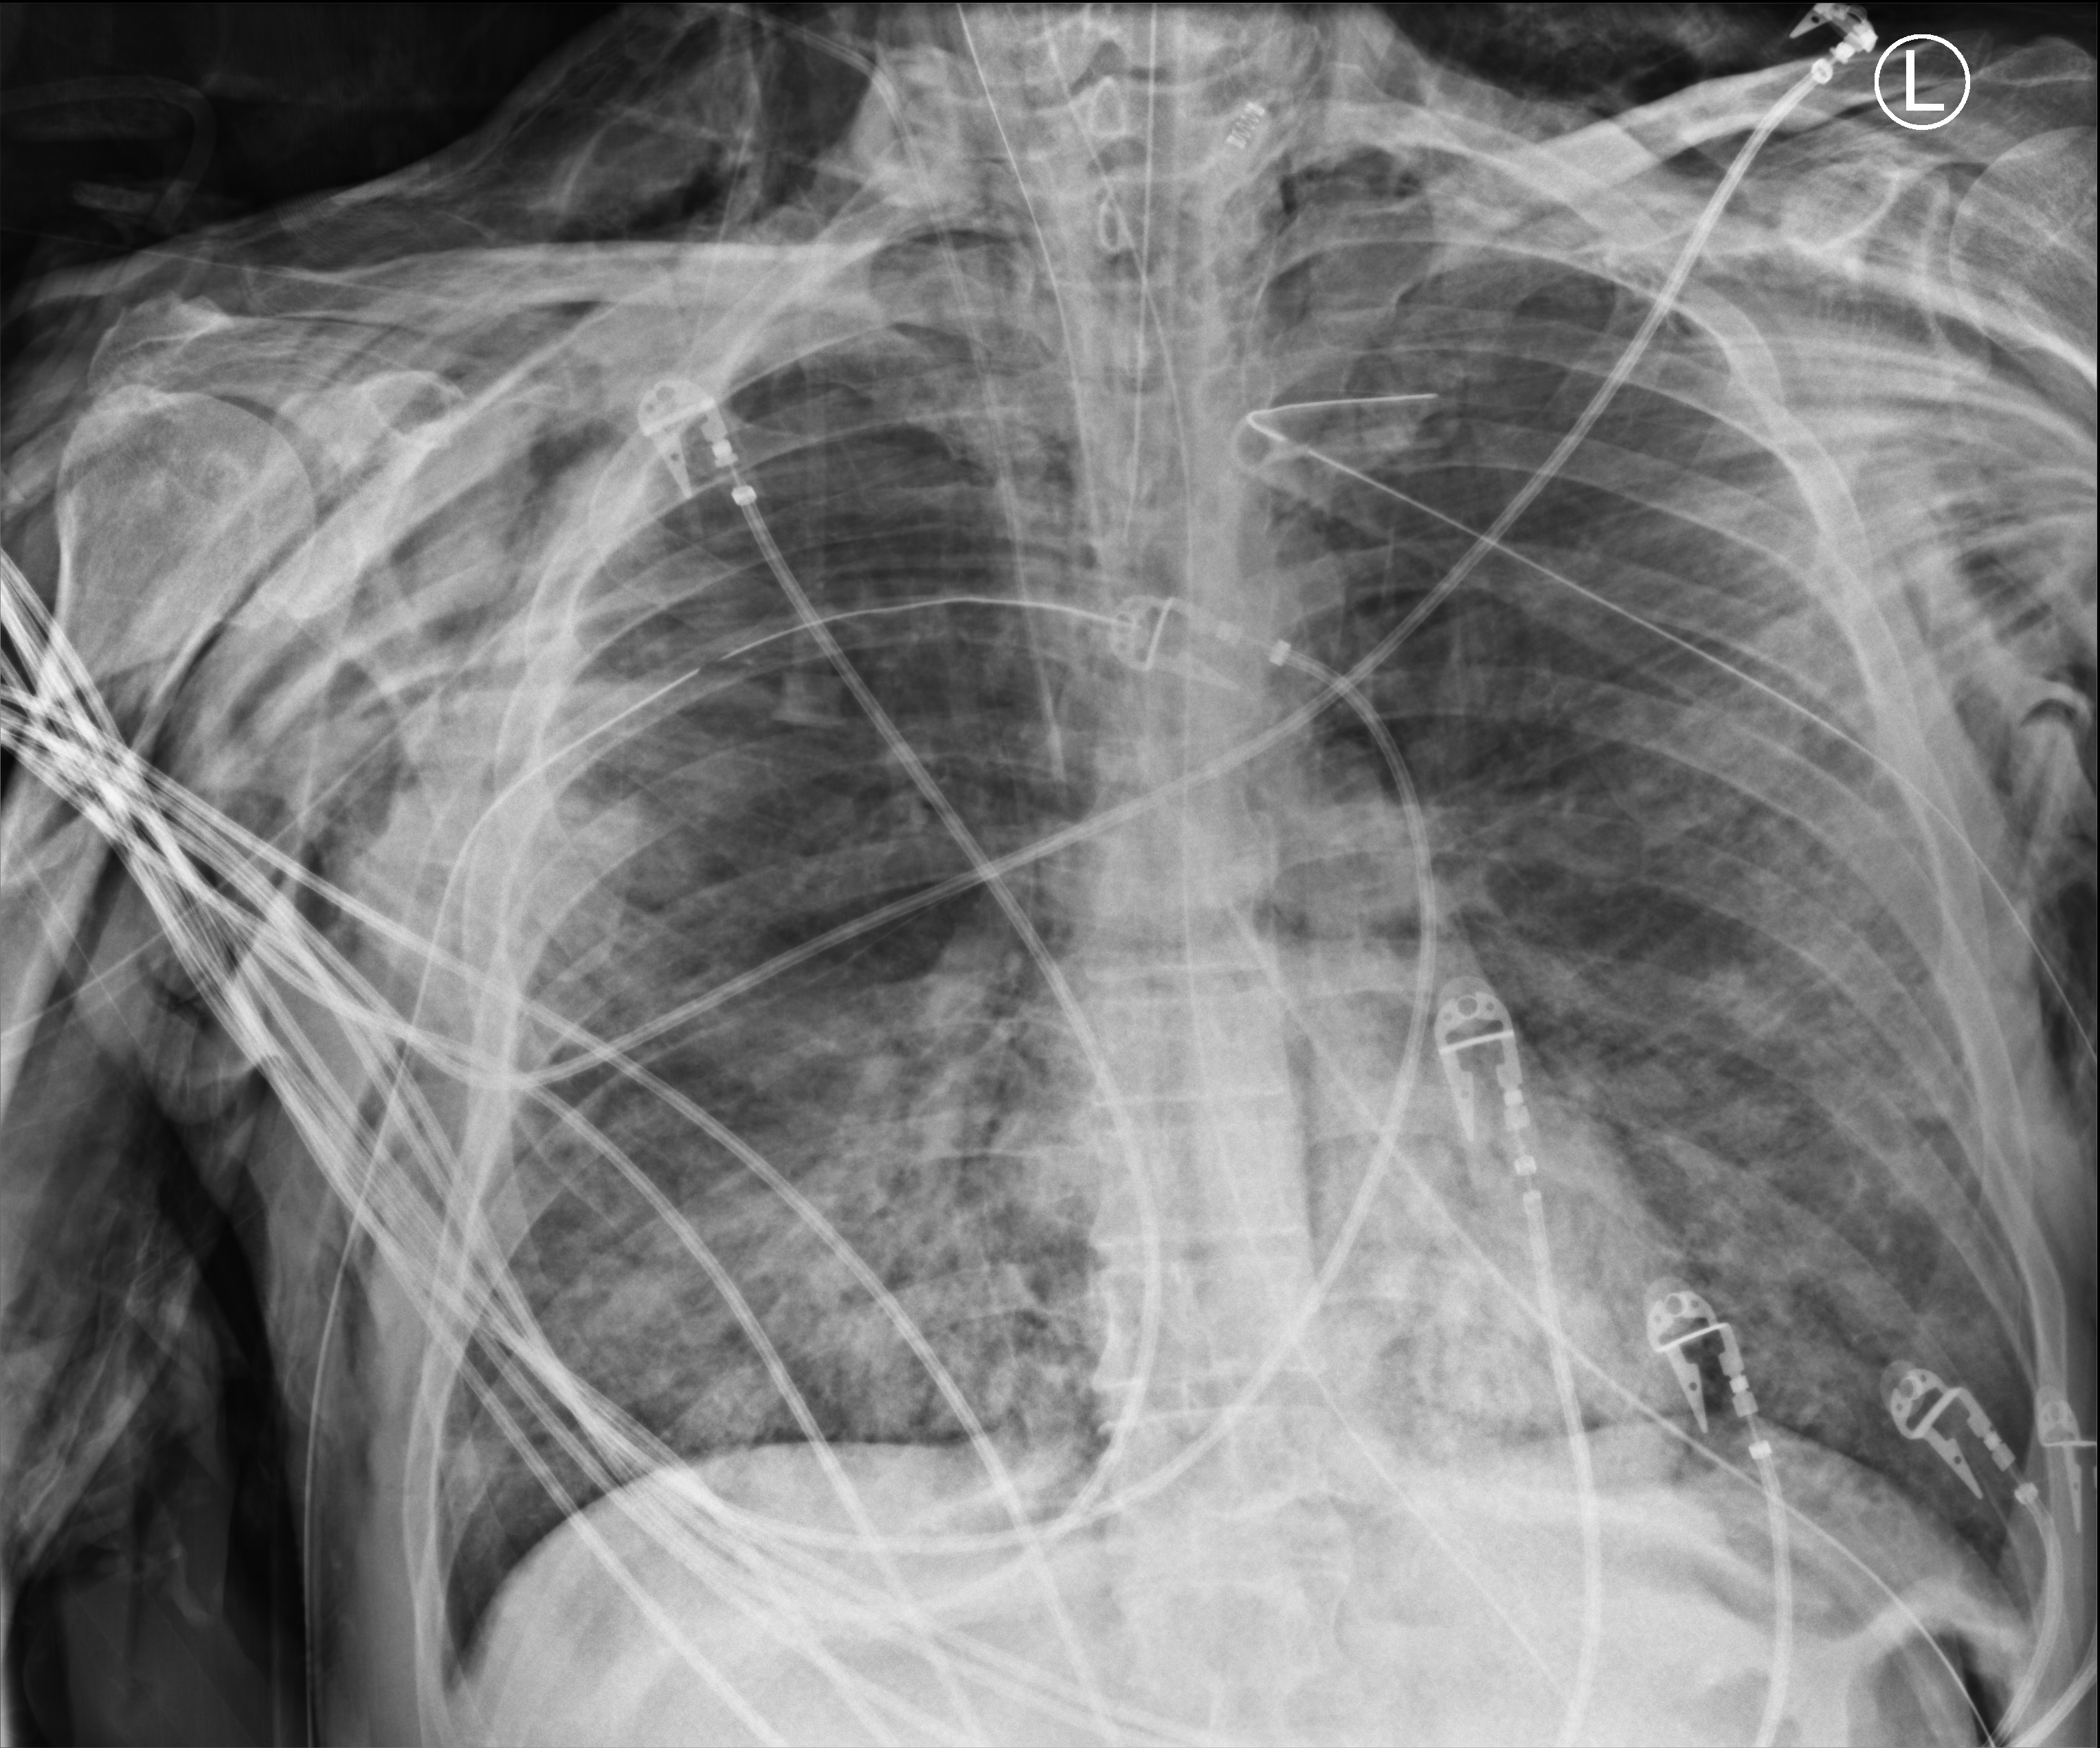
Portable chest radiograph. Male patient hospitalised with COVID-19, age 18–59 years.
Admission-level facts for this patient (not findings on this image; timing relative to this image not recorded):
- admitted to intensive care during this hospital stay: yes
- mechanically ventilated during this hospital stay: yes
- length of hospital stay: 96 days